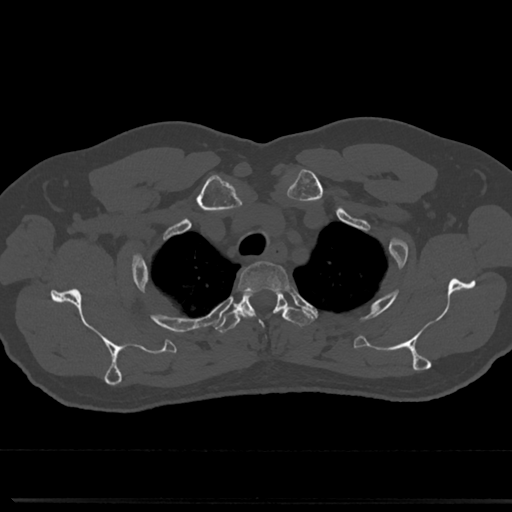
CT including the spine, one axial slice. Slice 610 of 817 in the series (ordered by position). Reconstruction kernel Br40s/3. Bone window (W 1800 / L 400 HU). 0.5 mm slice thickness. 512 × 512 image matrix, field of view 355 × 355 mm. Patient: male, 61 years. From the clinical record (not read from this slice): primary cancer: prostate.
Annotated regions visible in this slice (semi-automatic segmentation, software-assisted and operator-edited):
- T2 vertebra: bounding box <239,262,289,285> (left, top, right, bottom; pixels)
- T3 vertebra: <215,287,308,333>